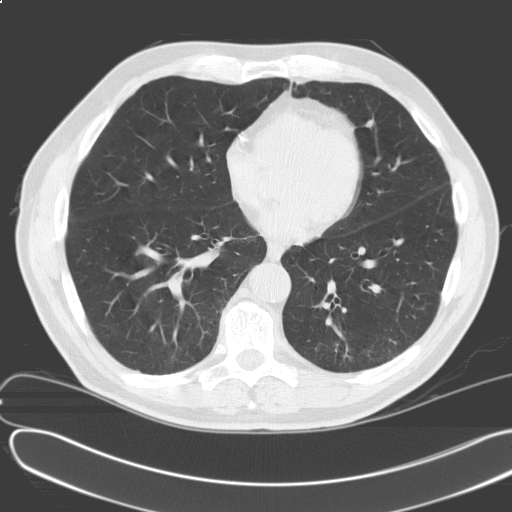
Chest CT (low-dose screening protocol), one axial image. Baseline annual screen. Lung window (W 1500 / L -600 HU). 3.2 mm slice thickness. Standard (soft-tissue) reconstruction kernel (C). Slice 65 of 164 in the series. Male, age 69 years at enrolment. Former smoker at enrolment.
Expert-annotated lung lesion, bounding box (x1, y1, x2, y2) in pixels: (210, 121, 240, 150). The screening reader recorded 2 non-calcified nodules or masses ≥4 mm on this exam (left upper lobe, right lower lobe); which of them this box marks is not recorded.